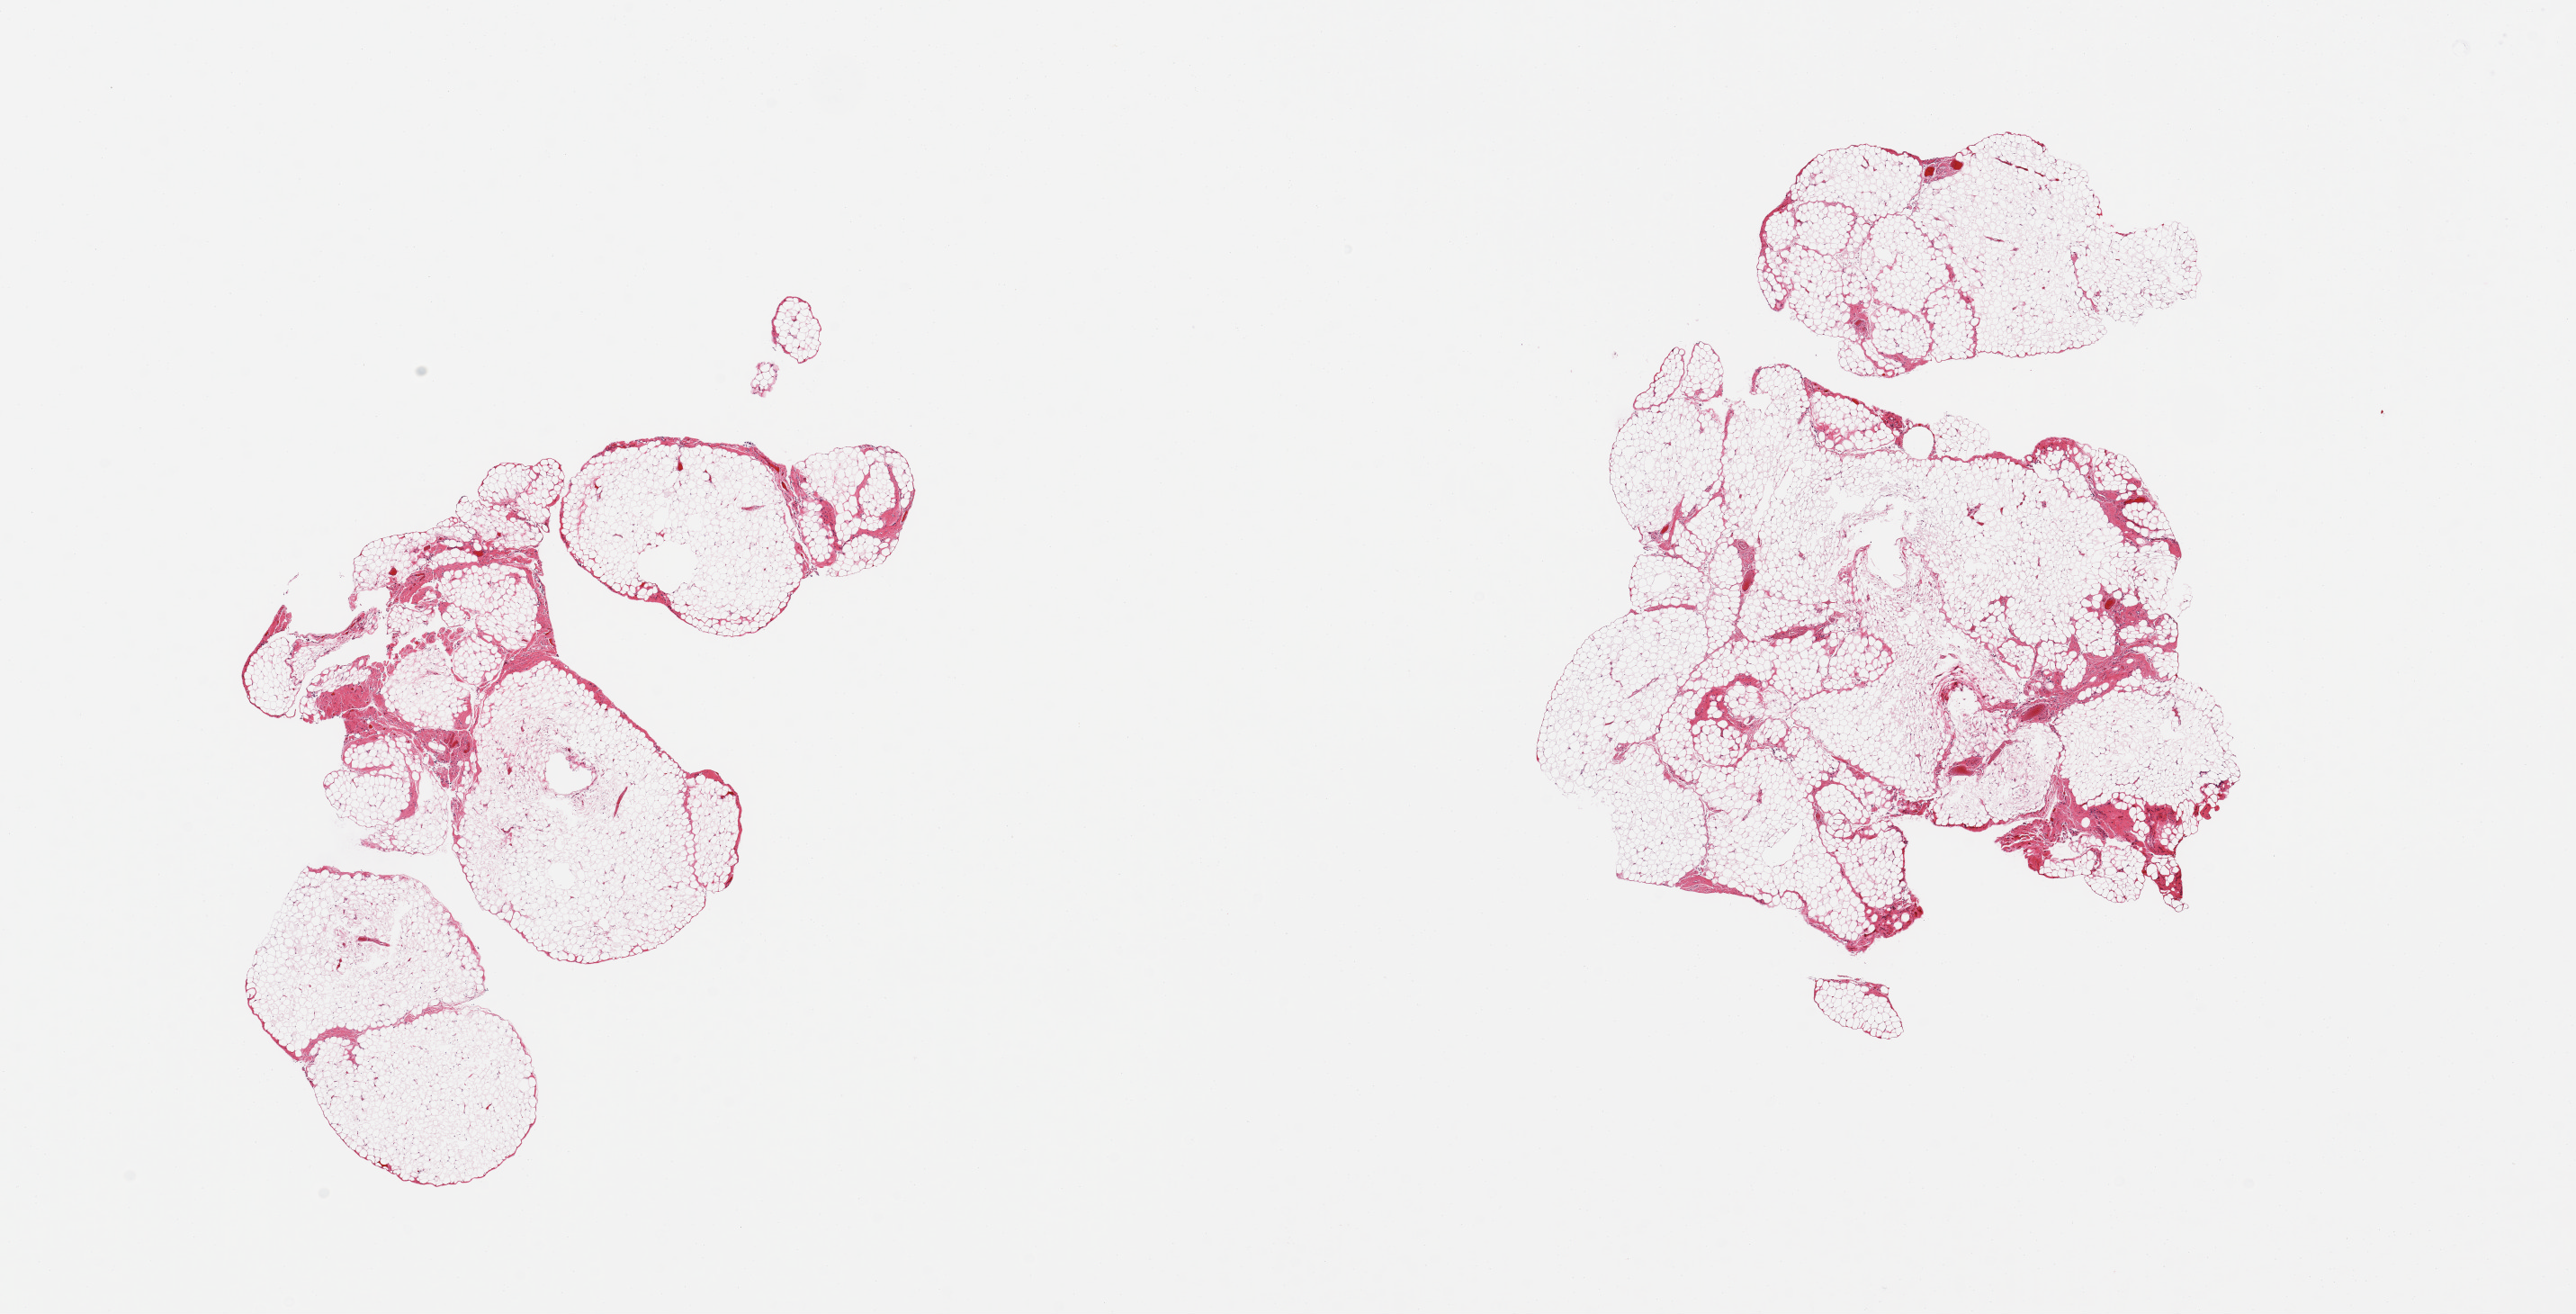
Whole-slide image, hematoxylin and eosin (H&E) stain — shown as a low-resolution overview of the whole scanned area (about 22.6 x 11.5 mm); PAXgene-fixed, paraffin-embedded tissue; sampled site (target tissue): omentum; donor tissue sample. Donor: female.
Pathologist's review note for this sample: 2 pieces; lobulated mature fat, <10% fibrous tissue.